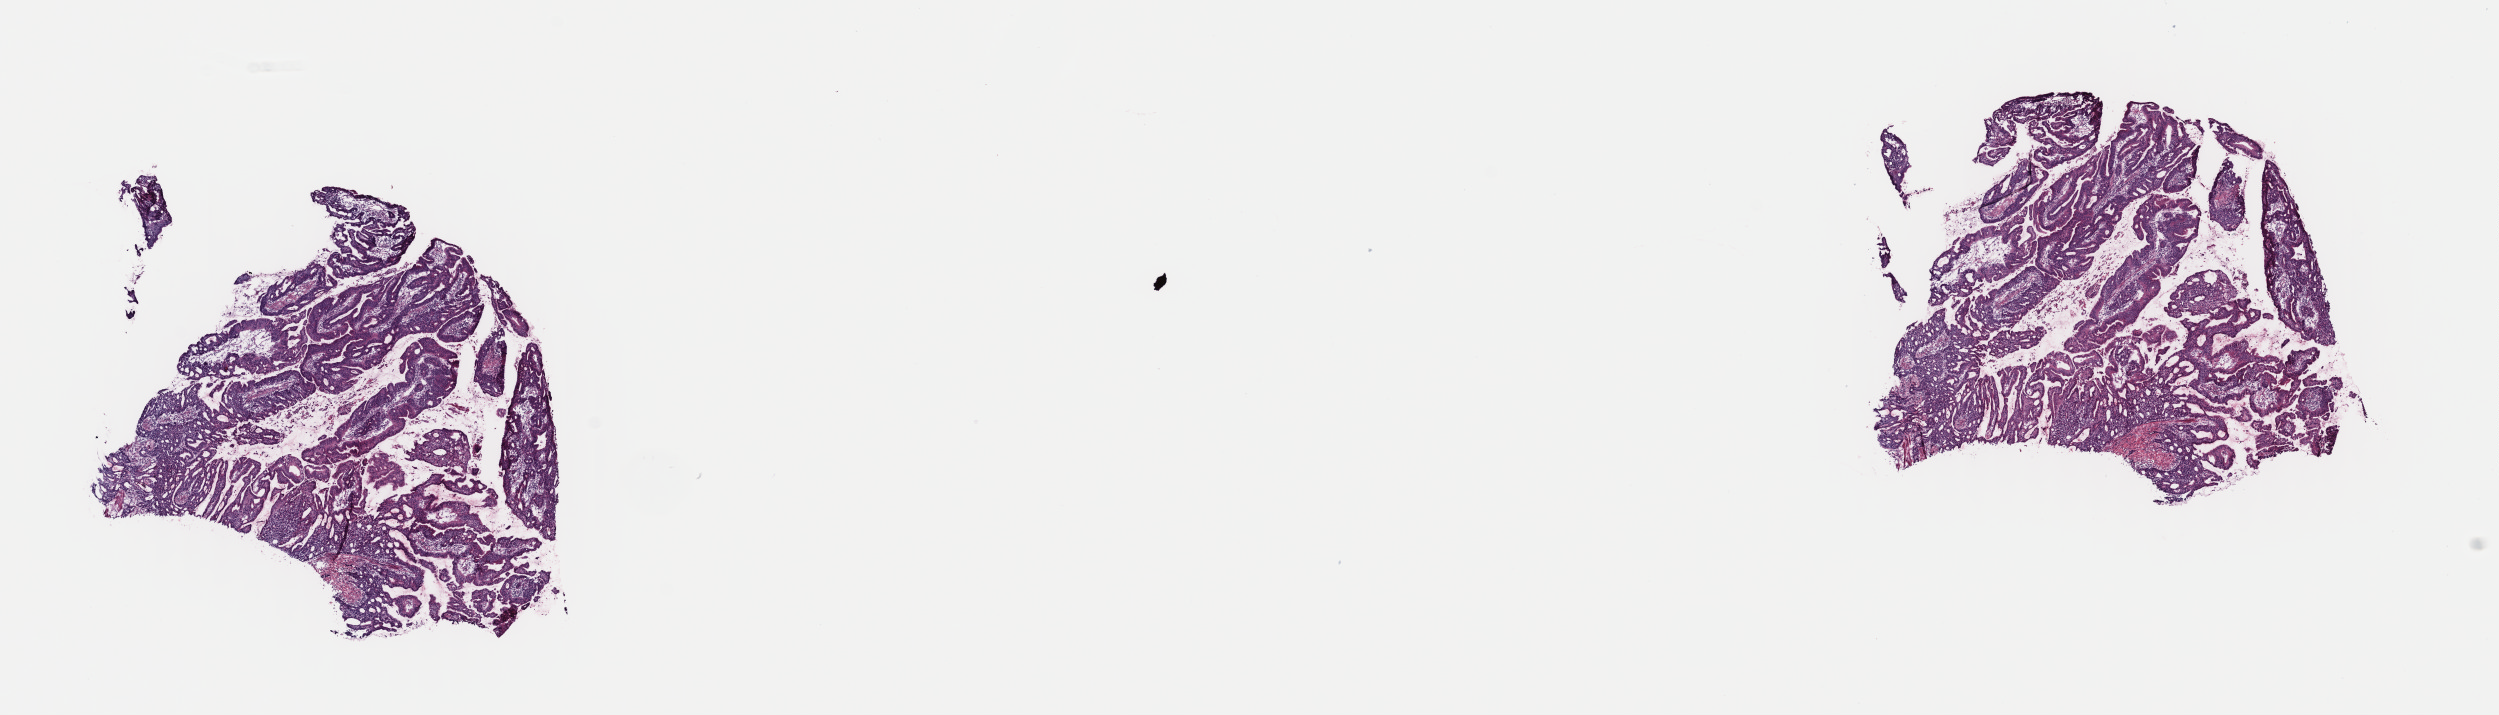
Digitized Hematoxylin and eosin (H&E) stained tissue section (whole slide) — low-resolution overview of the scanned area, about 19.7 x 5.6 mm (from a 40x scan), frozen section from the top of the tissue portion, primary tumour sample from the stomach. Female patient; age at initial diagnosis 61 years. Histologic grade: G2 (moderately differentiated). Composition of this section per pathologist review: tumour cells 85%, tumour nuclei 95%, normal cells 0%, stromal cells 15%, necrosis 0%. Infiltration values recorded for this section: lymphocyte infiltration 0%, monocyte infiltration 0%, neutrophil infiltration 0%.
Histologic diagnosis: Adenocarcinoma, intestinal type (cardia, NOS). AJCC pathologic stage: IIIA (7th edition).